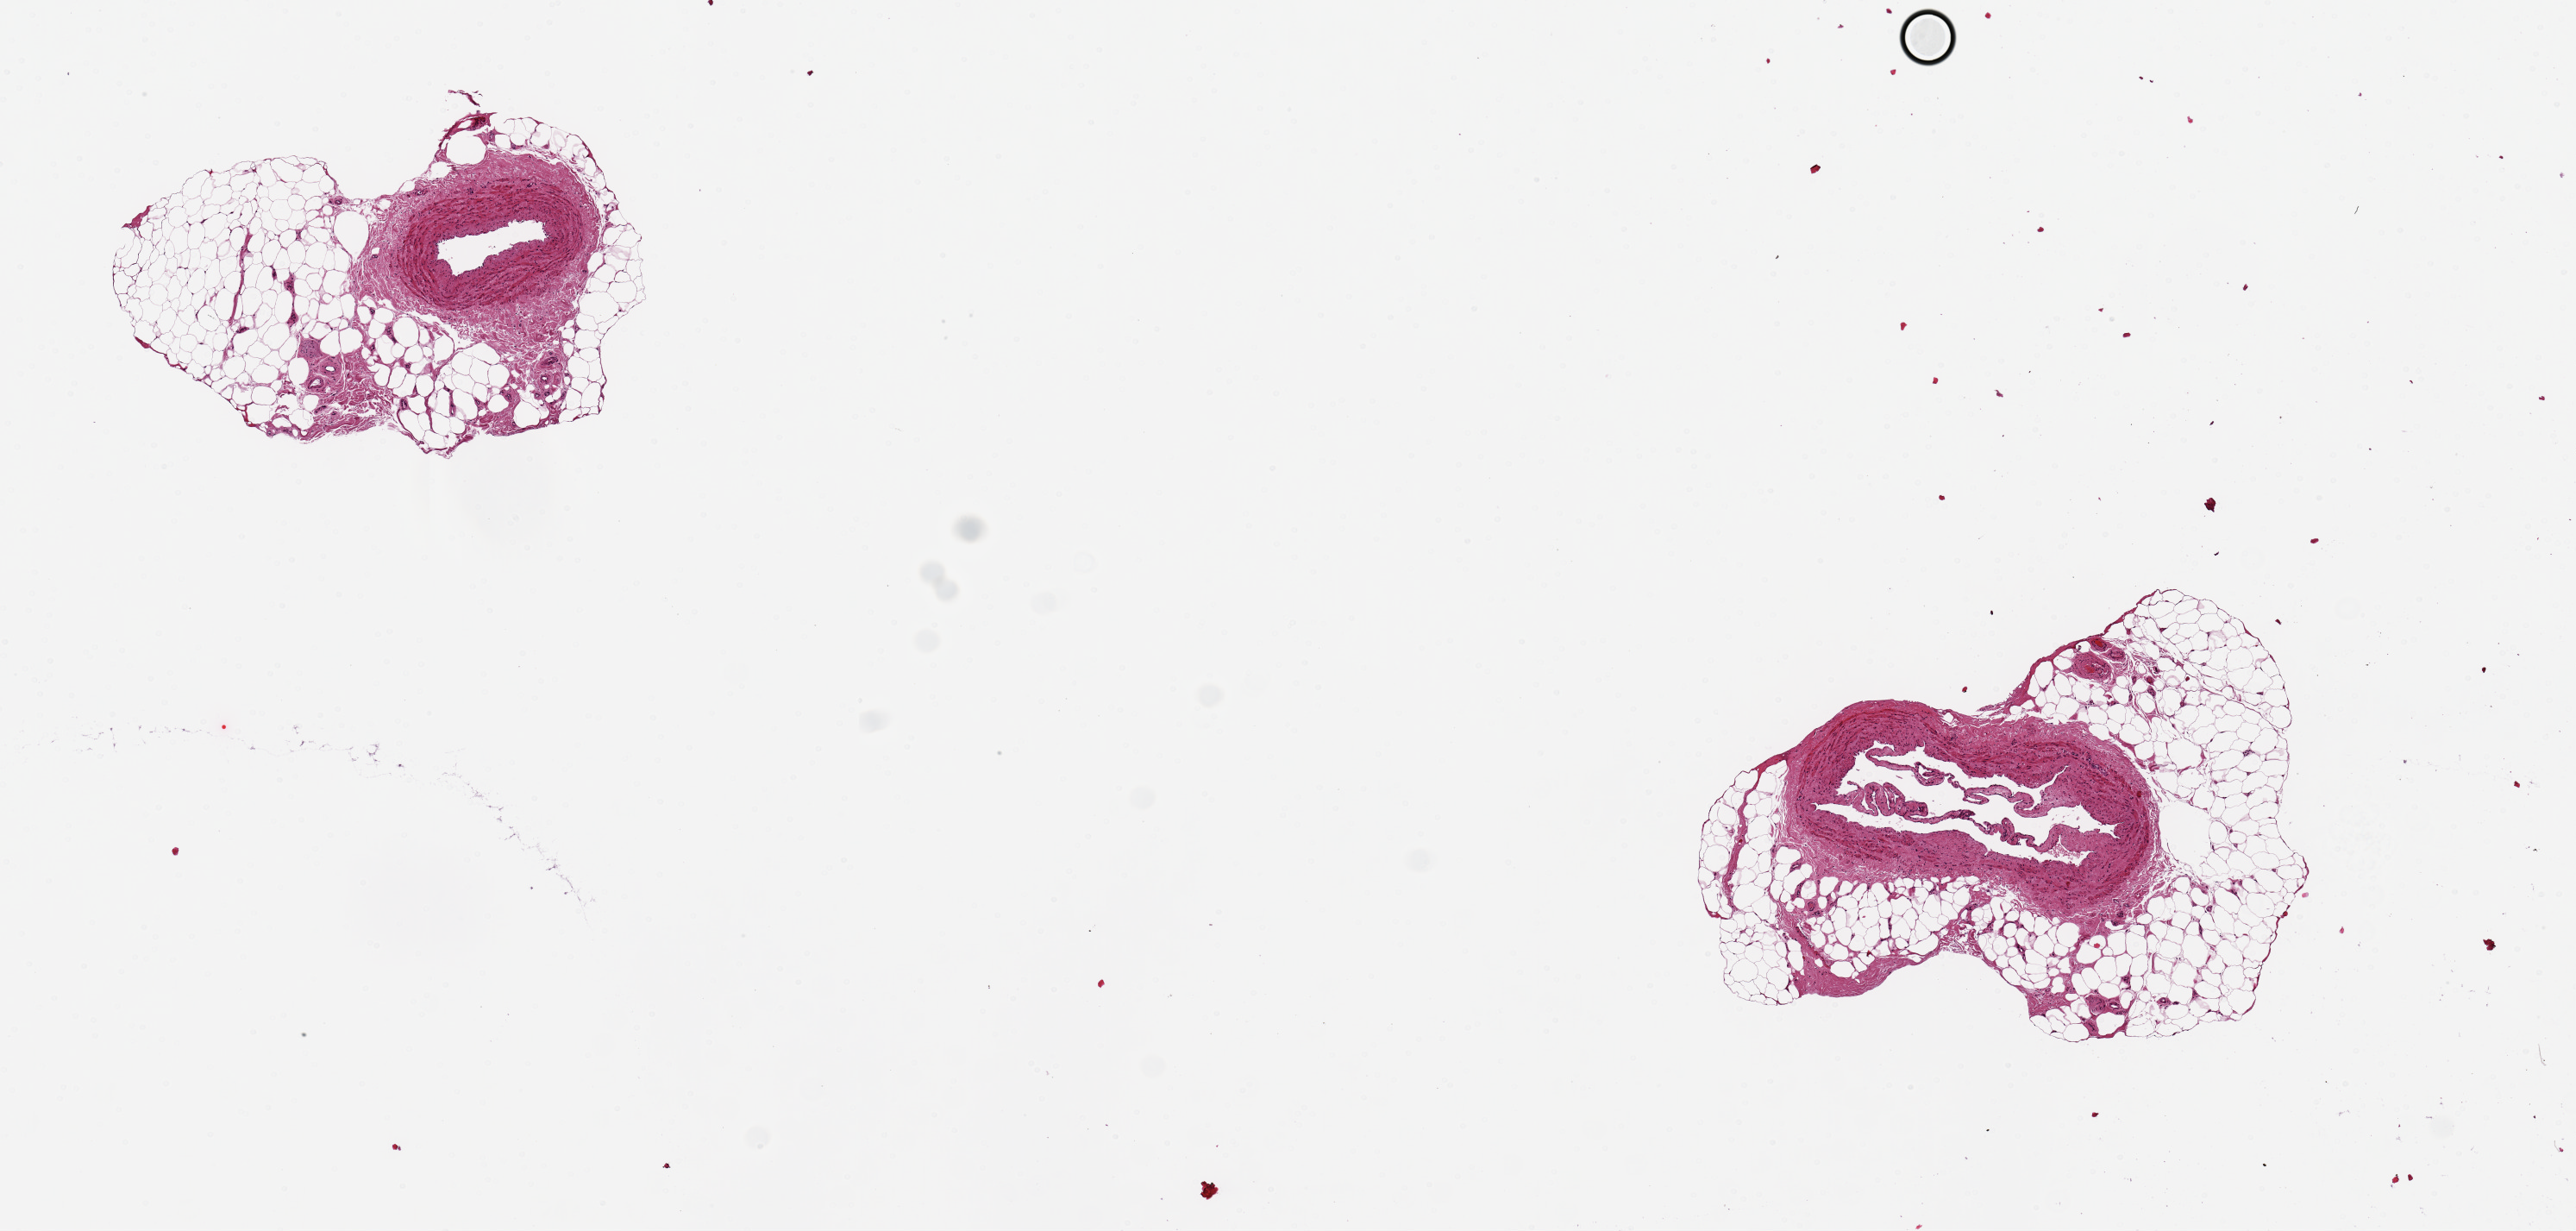
Hematoxylin and eosin (H&E) whole-slide image, brightfield — shown as a low-resolution overview of the whole scanned area (about 11.8 x 5.6 mm, acquisition: 20x scan), PAXgene-fixed, paraffin-embedded tissue, target tissue: tibial artery, donor tissue sample. Donor sex: female.
Pathologist's review note for this sample: 2 pieces, 2x1 & 2.5x2mm; one artery, one vein; ~50% adipose encasing vessels.